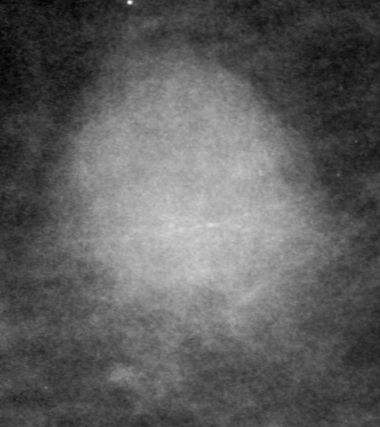
Cropped region of a digitized screen-film mammogram centred on a radiologist-marked abnormality, right breast, CC view, BI-RADS breast density category 2 (scale 1–4).
Mass, shape round, margins ill defined; BI-RADS assessment category 5; subtlety rating 5 on a 1 (subtle) to 5 (obvious) scale; pathology (as recorded): malignant.